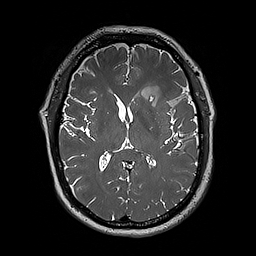
Brain MRI from a brain-tumour surgery series, one axial slice. 1 mm slice thickness. 256 × 256 image matrix, field of view 250 × 250 mm. Case-level facts recorded for this patient, not image findings: histopathology: Oligodendroglioma; WHO grade: 3; IDH mutation: yes.
Outlined on this slice (outlined manually by an expert reader):
- tumour: box from (x=142, y=82) to (x=188, y=117) px